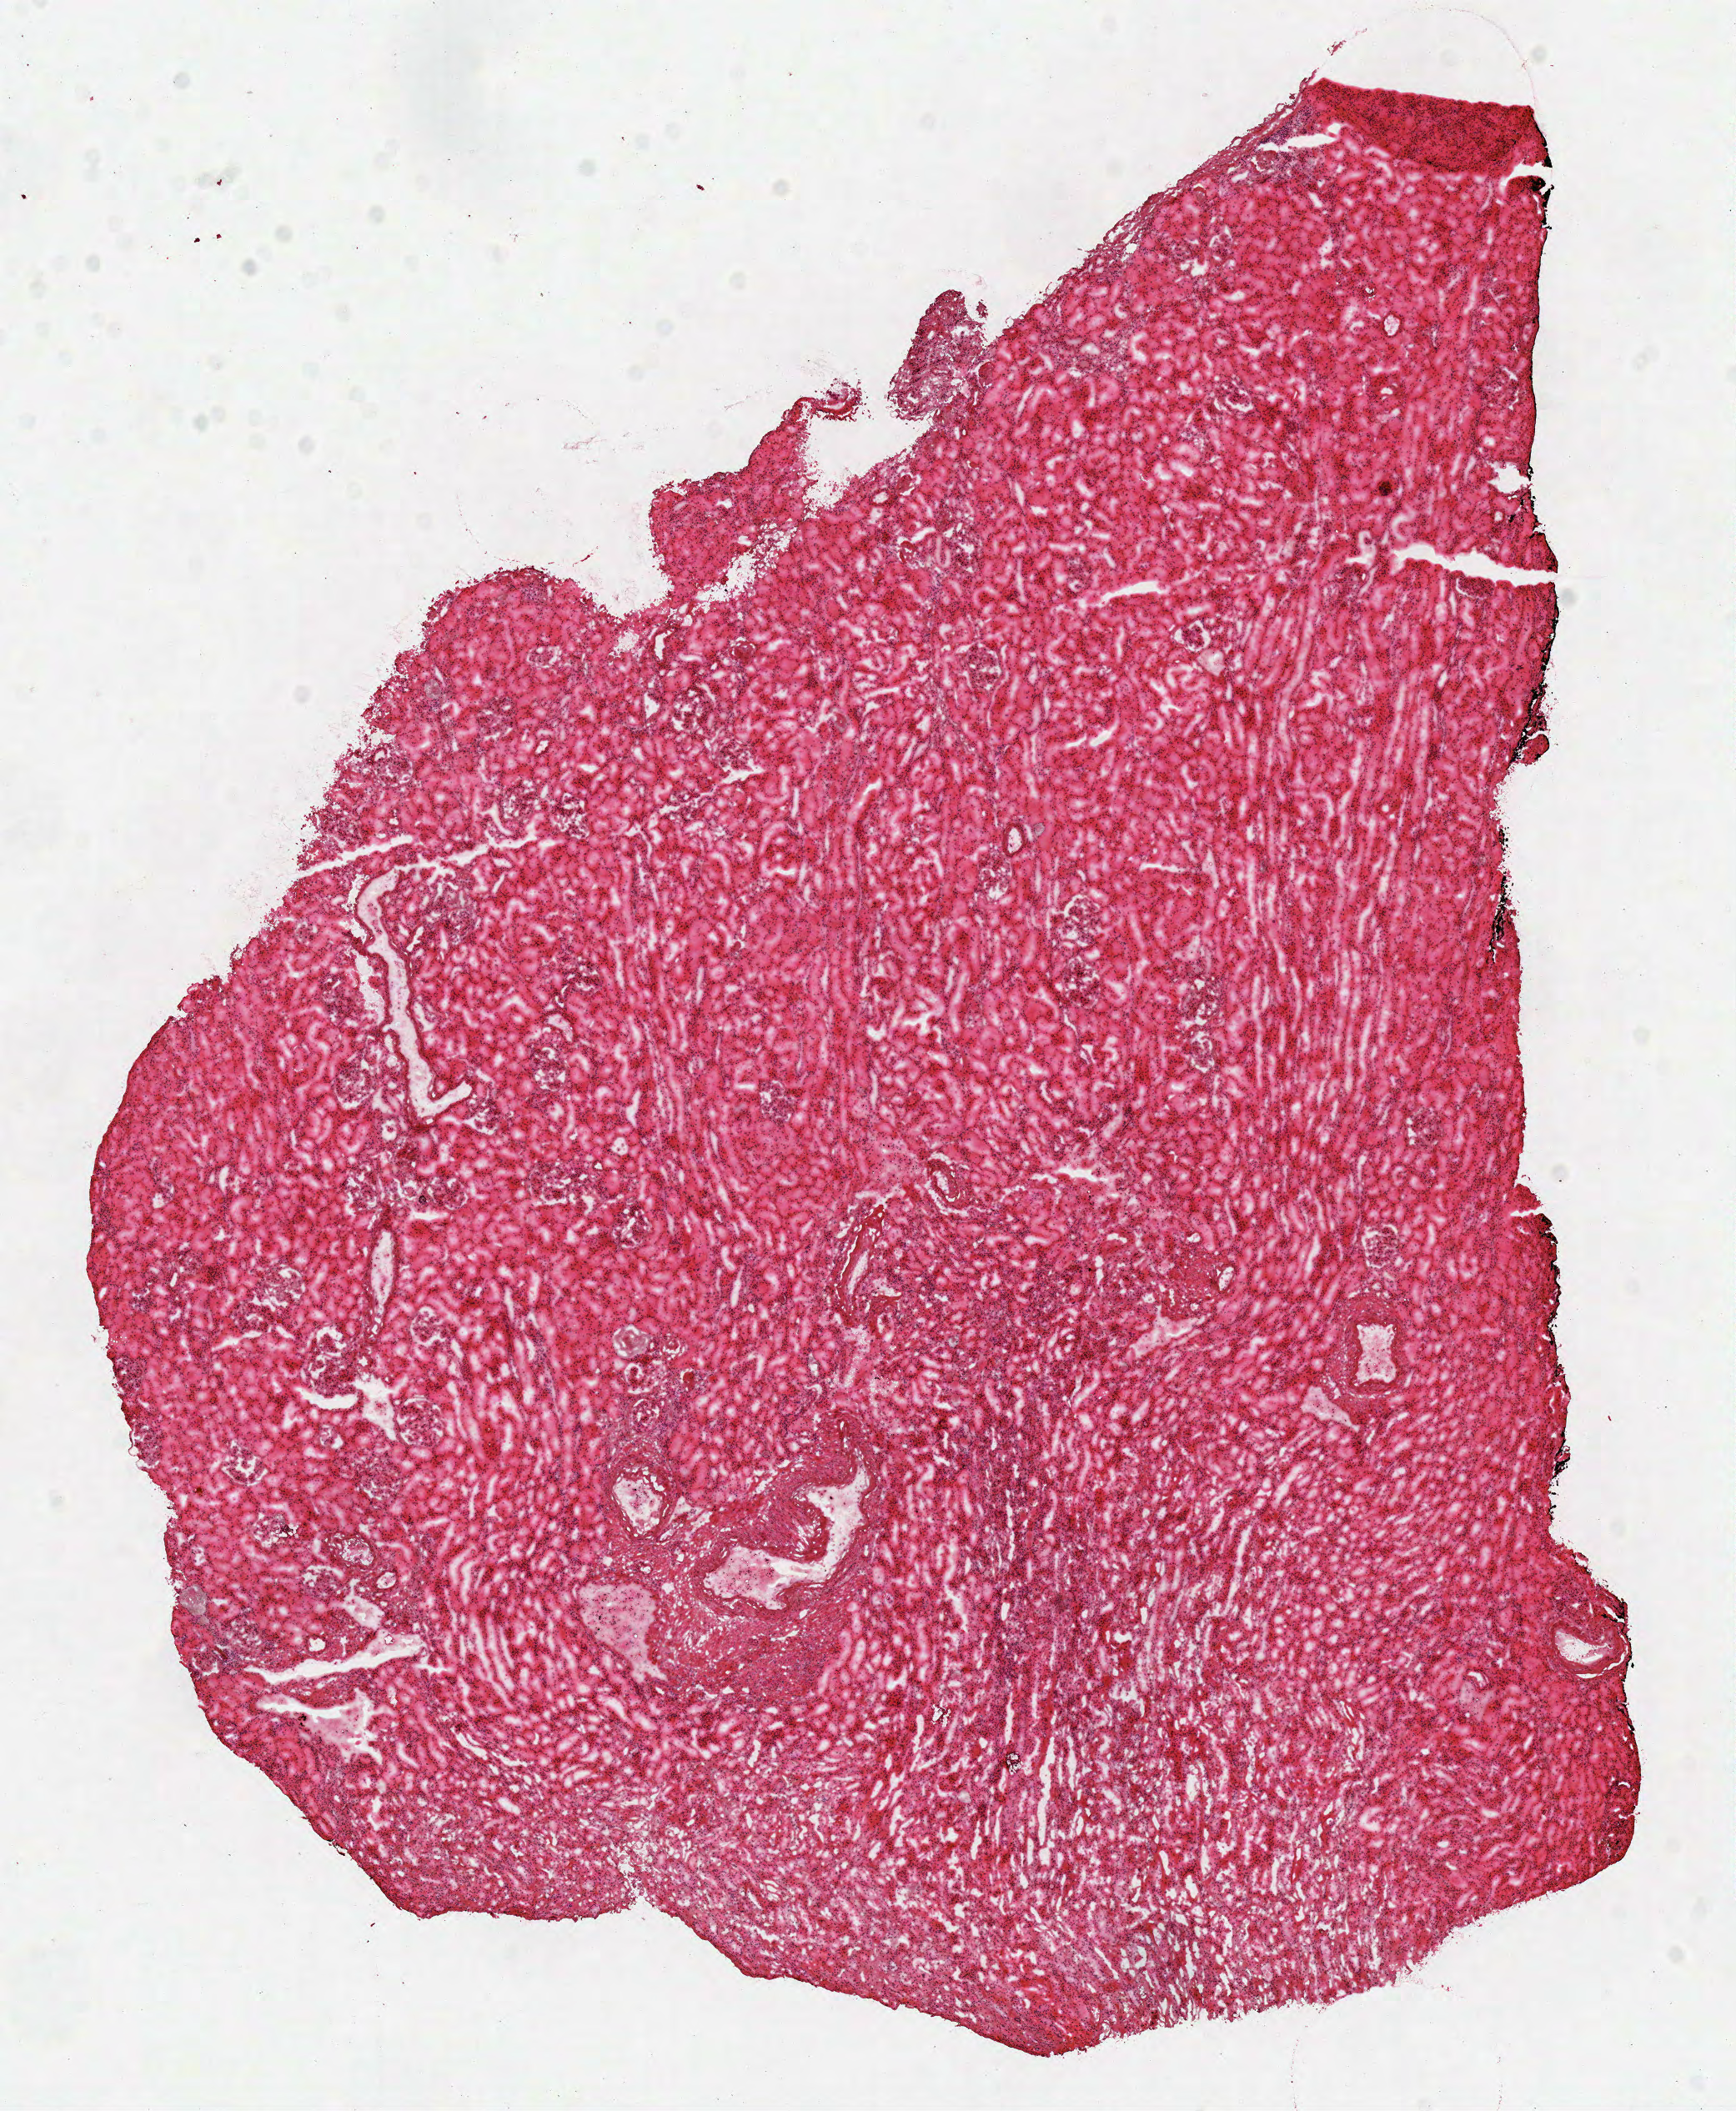
H&E whole-slide image — low-resolution overview of the scanned area, about 8.2 x 10.0 mm (slide scanned at 40x); frozen section; sample: solid tissue normal (non-tumour tissue), kidney. Male, age 75 years at initial diagnosis.
* this section: solid tissue normal (non-tumour) sample from the same patient
* patient diagnosis: Papillary adenocarcinoma, NOS